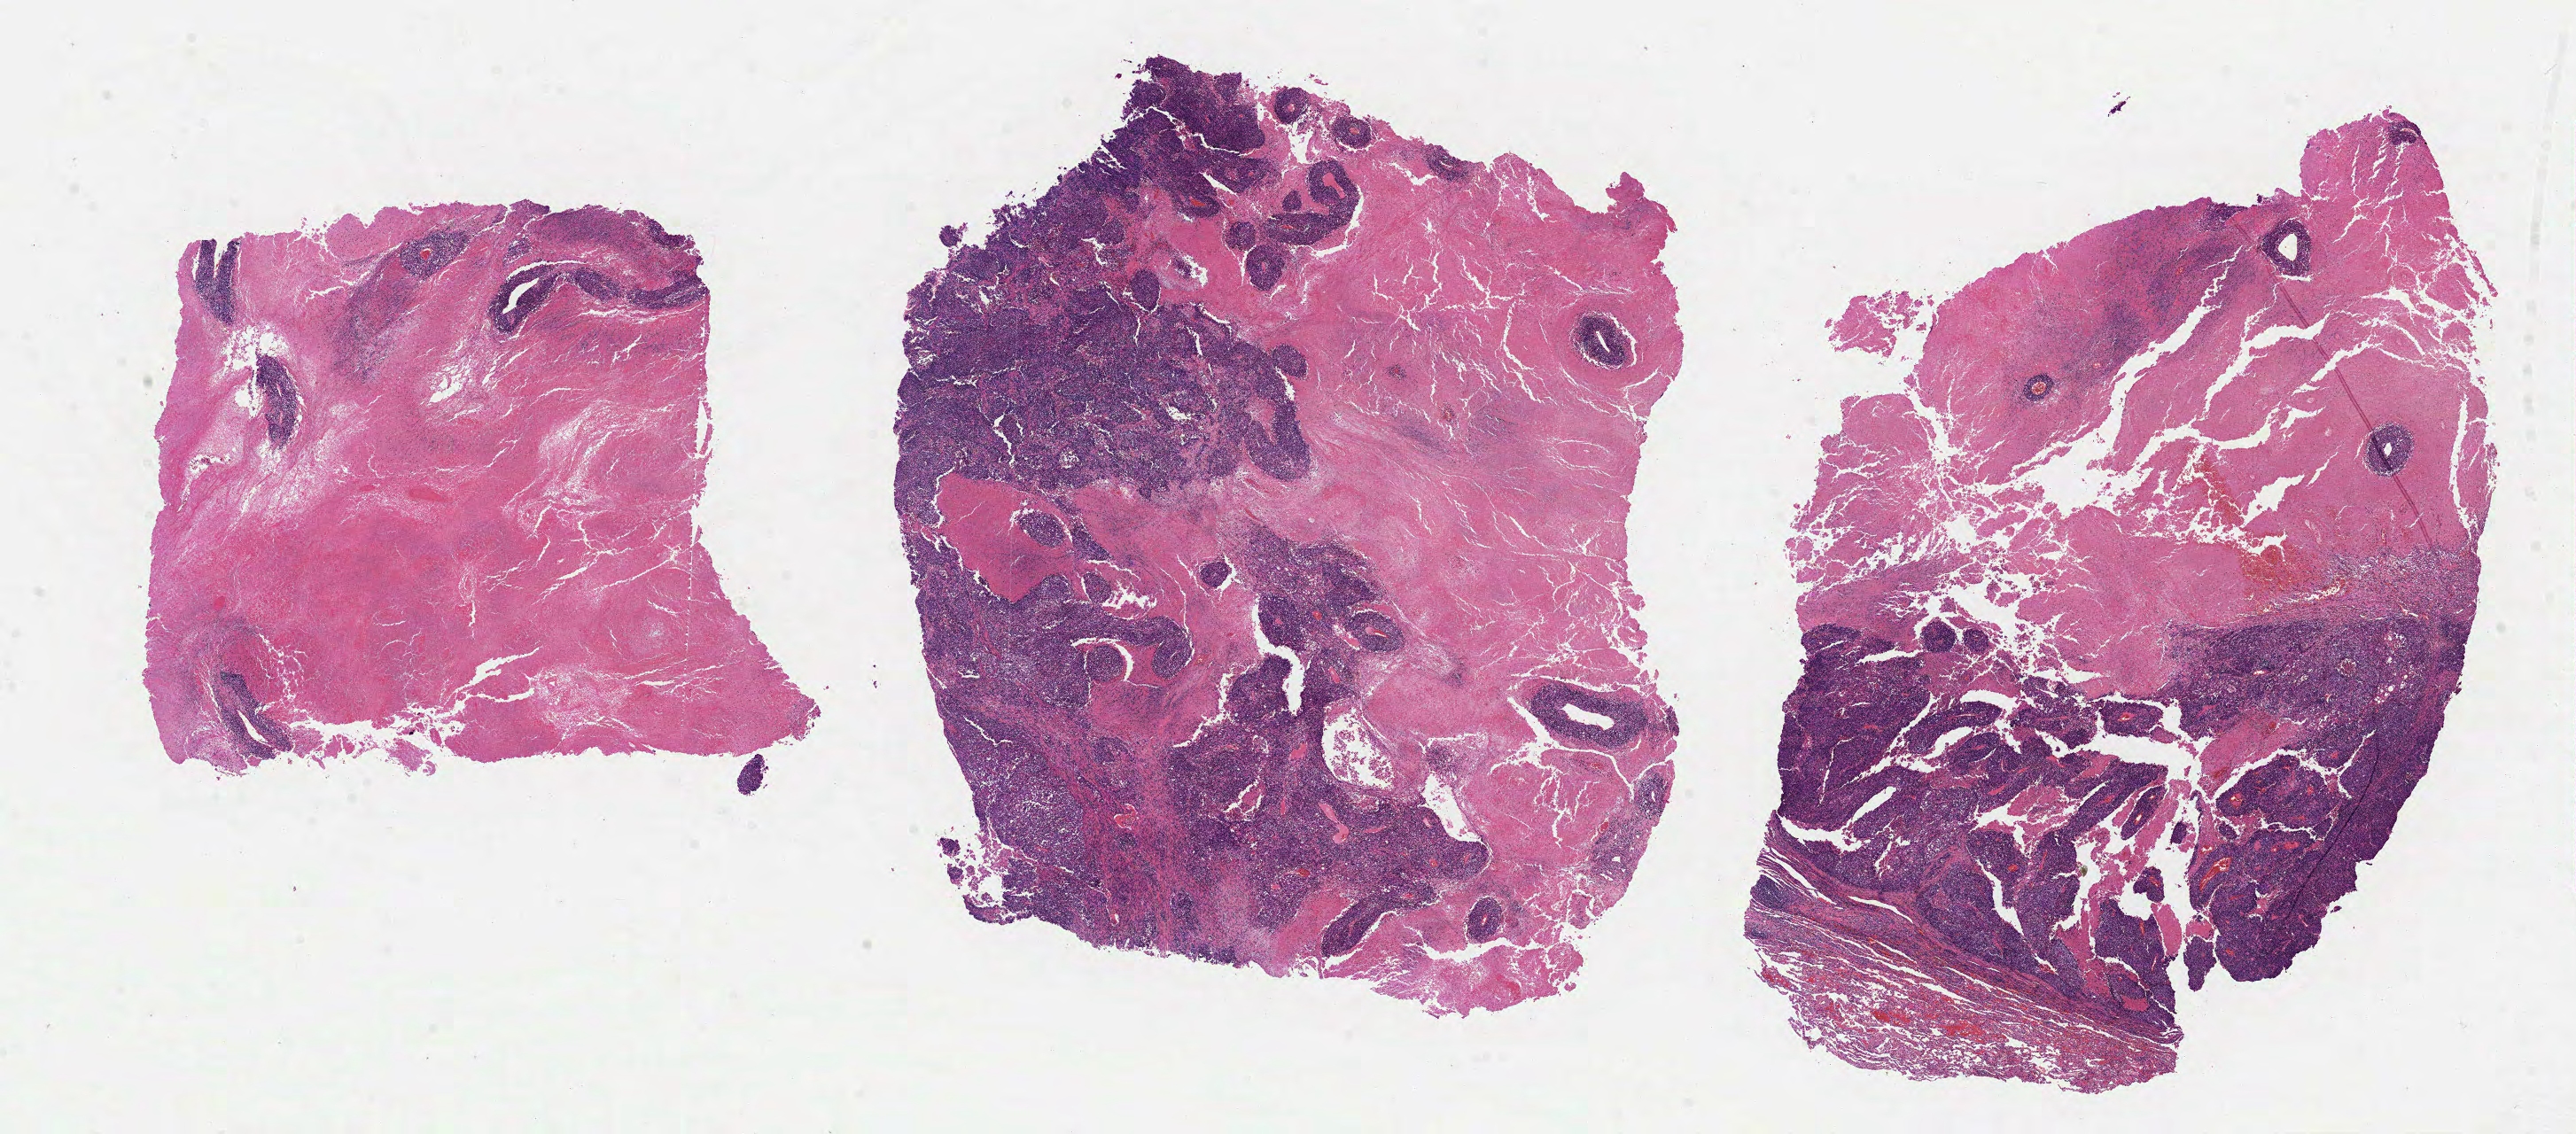
Whole-slide histology image, Hematoxylin and eosin (H&E) stained, a low-resolution overview of the entire scanned area, about 23.4 x 10.3 mm (from a 40x scan). Formalin-fixed paraffin-embedded (FFPE) diagnostic section. Primary tumour sample from the lung. Female, age 65 years at initial diagnosis.
• laterality: right
• pathologic diagnosis: Squamous cell carcinoma, NOS (upper lobe, lung)
• AJCC pathologic stage: IA (7th edition)